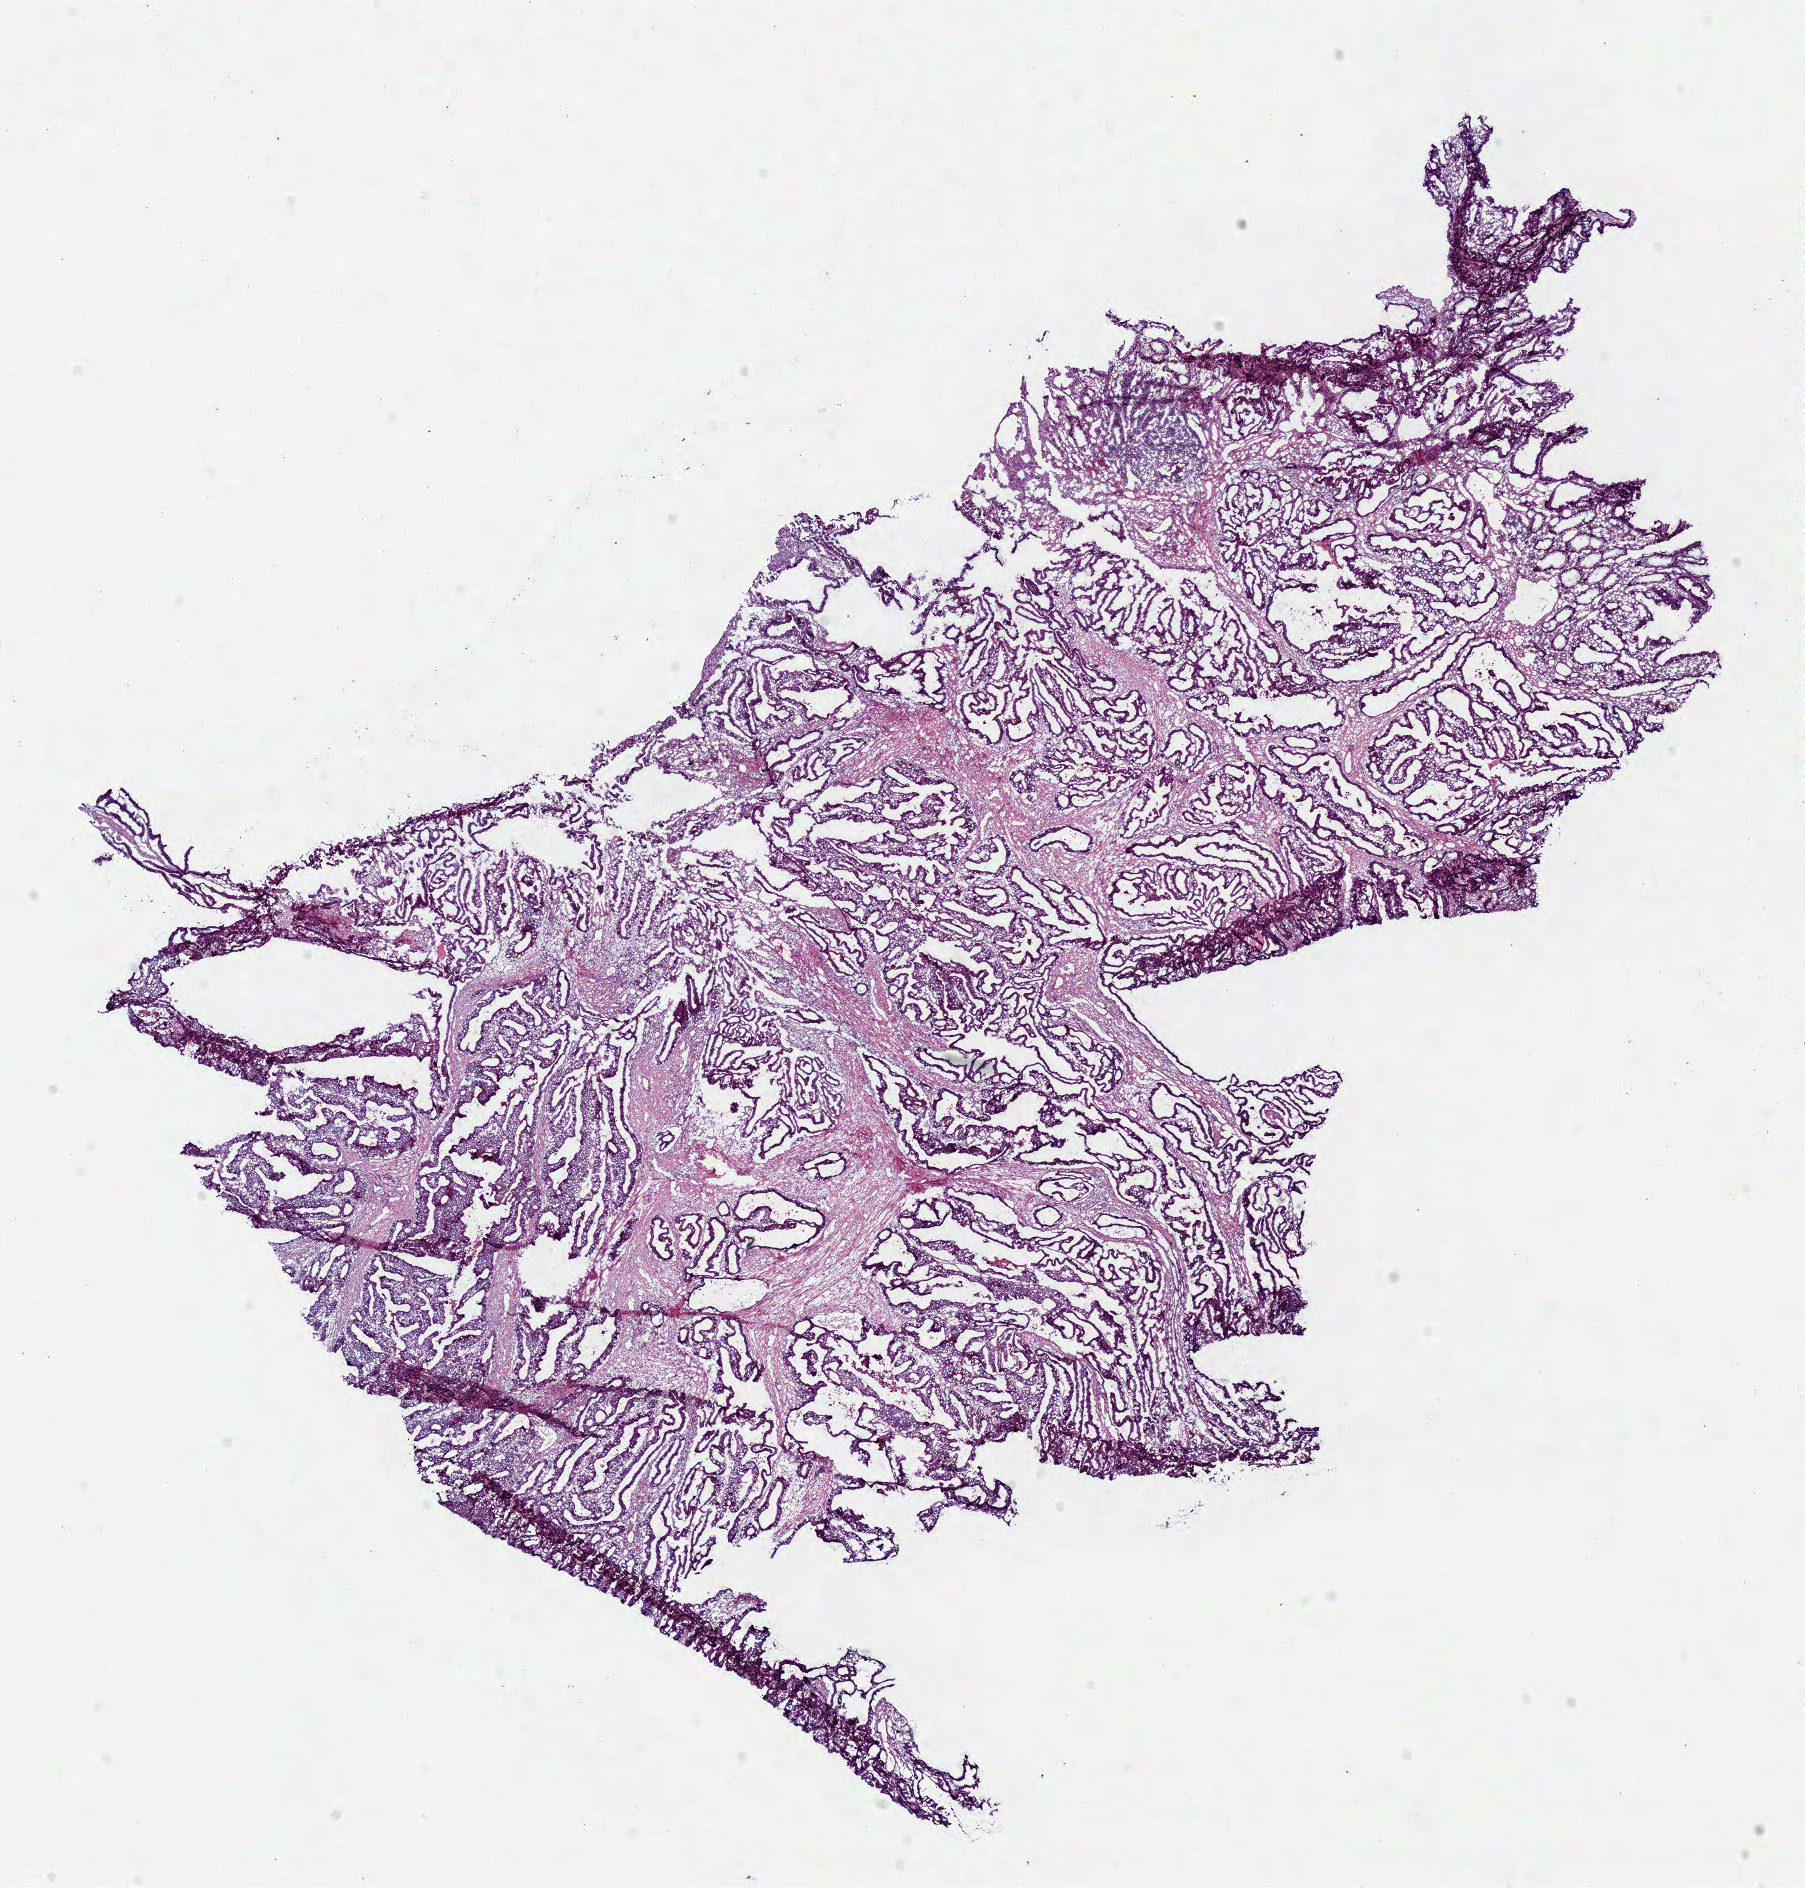
H&E-stained whole-slide image, shown as a low-resolution overview of the whole scanned area (about 14.2 x 14.8 mm, from a 40x scan), frozen section from the bottom of the tissue portion, primary tumour sample from the colon. Patient: female, age at initial diagnosis 37 years. Pathologist review of this section (percent, as recorded): tumour cells 78%, tumour nuclei 80%, normal cells 5%, stromal cells 12%, necrosis 5%.
TNM: T3 N1 M0. Histologic diagnosis: Adenocarcinoma, NOS (sigmoid colon). Lymph nodes positive (case pathology): 2 of 17 examined. AJCC pathologic stage: IIIB.